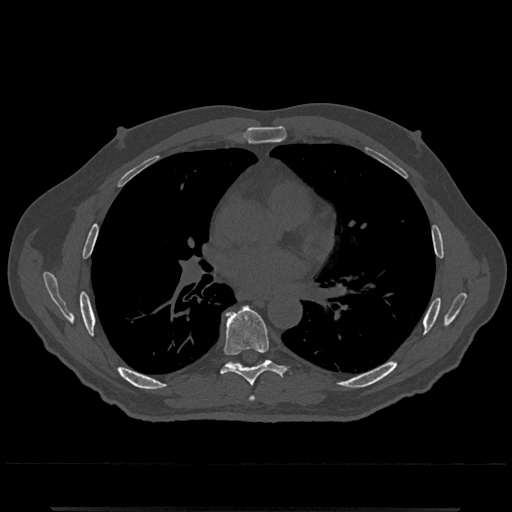
CT including the spine, one axial slice. Position 718 of 797 along the scan axis. 120 kVp. Bone window (W 1800 / L 400 HU). 0.5 mm slice thickness. 512 × 512 image matrix, field of view 393 × 393 mm. Patient: male, 67 years. From the clinical record (not read from this slice): primary cancer: prostate.
Outlined on this slice (semi-automatic segmentation, software-assisted and operator-edited):
- T6 vertebra: box from (x=249, y=396) to (x=255, y=402) px
- T7 vertebra: (x=221, y=306)–(x=284, y=387)